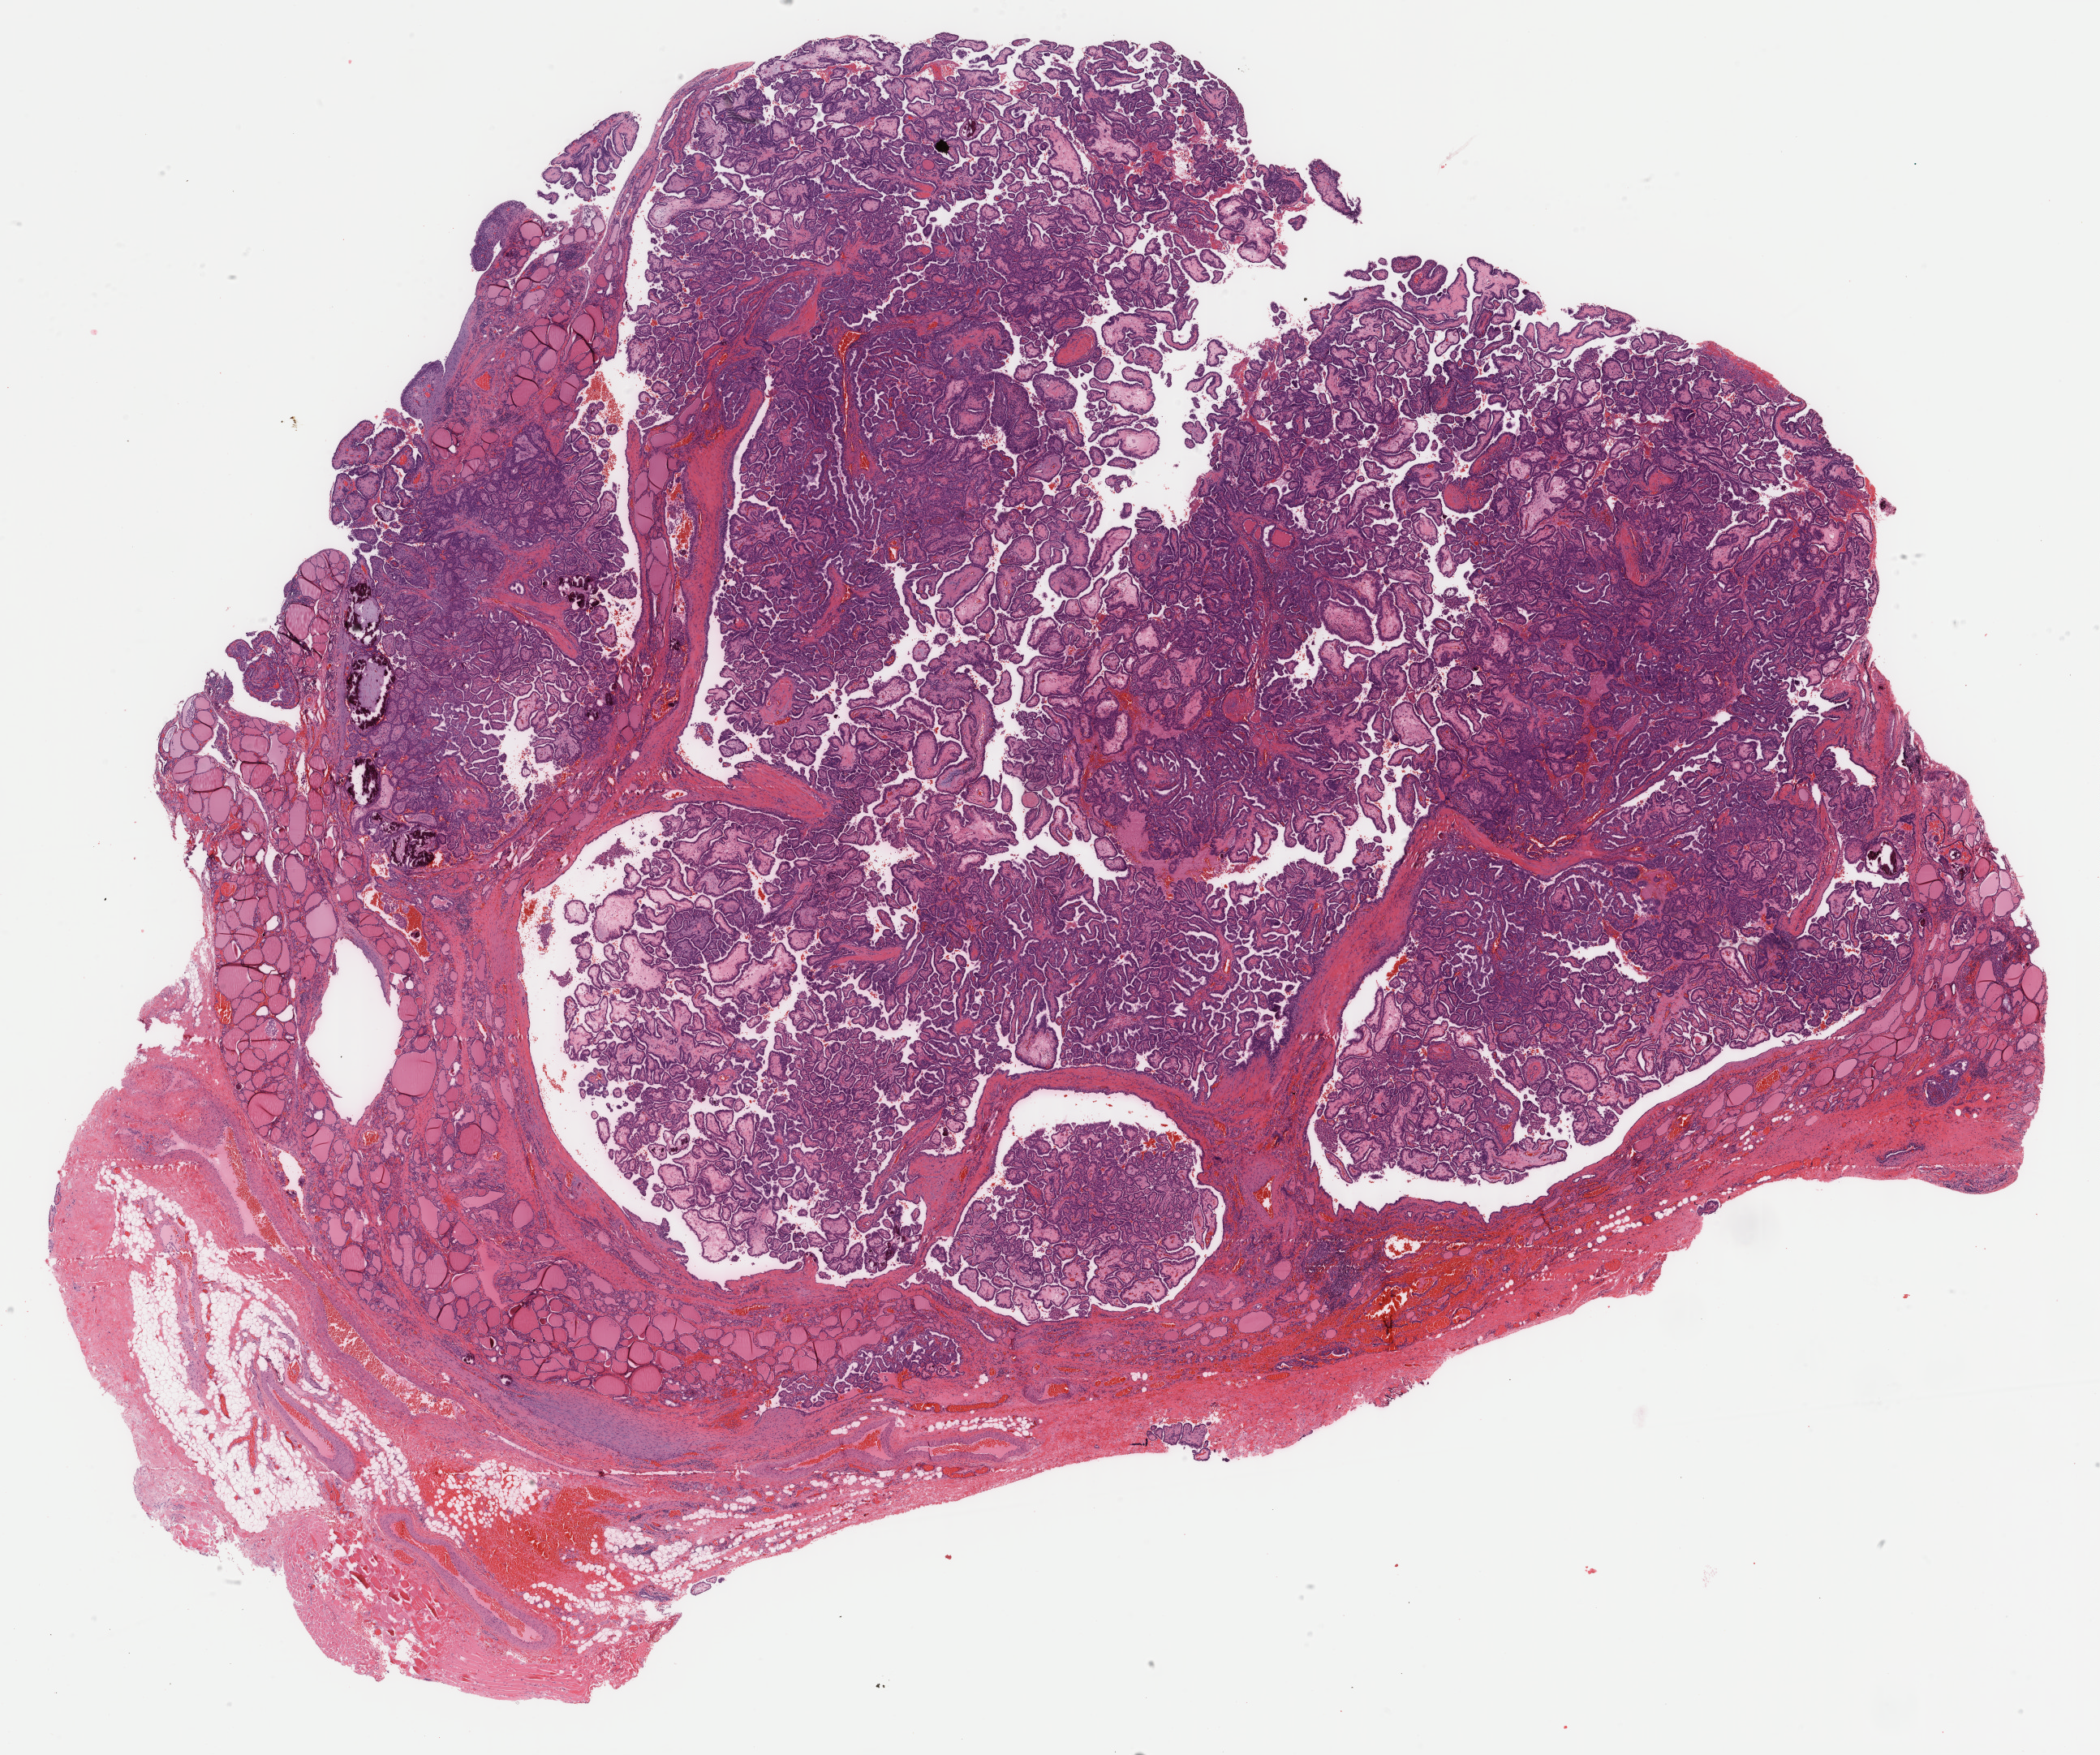
Whole-slide histology image, H&E, a low-resolution overview of the entire scanned area, about 20.5 x 17.2 mm, formalin-fixed paraffin-embedded (FFPE) diagnostic section, primary tumour sample from the thyroid. Female, age 31 years at initial diagnosis.
• histologic diagnosis: Papillary adenocarcinoma, NOS
• laterality: right
• AJCC pathologic stage: I